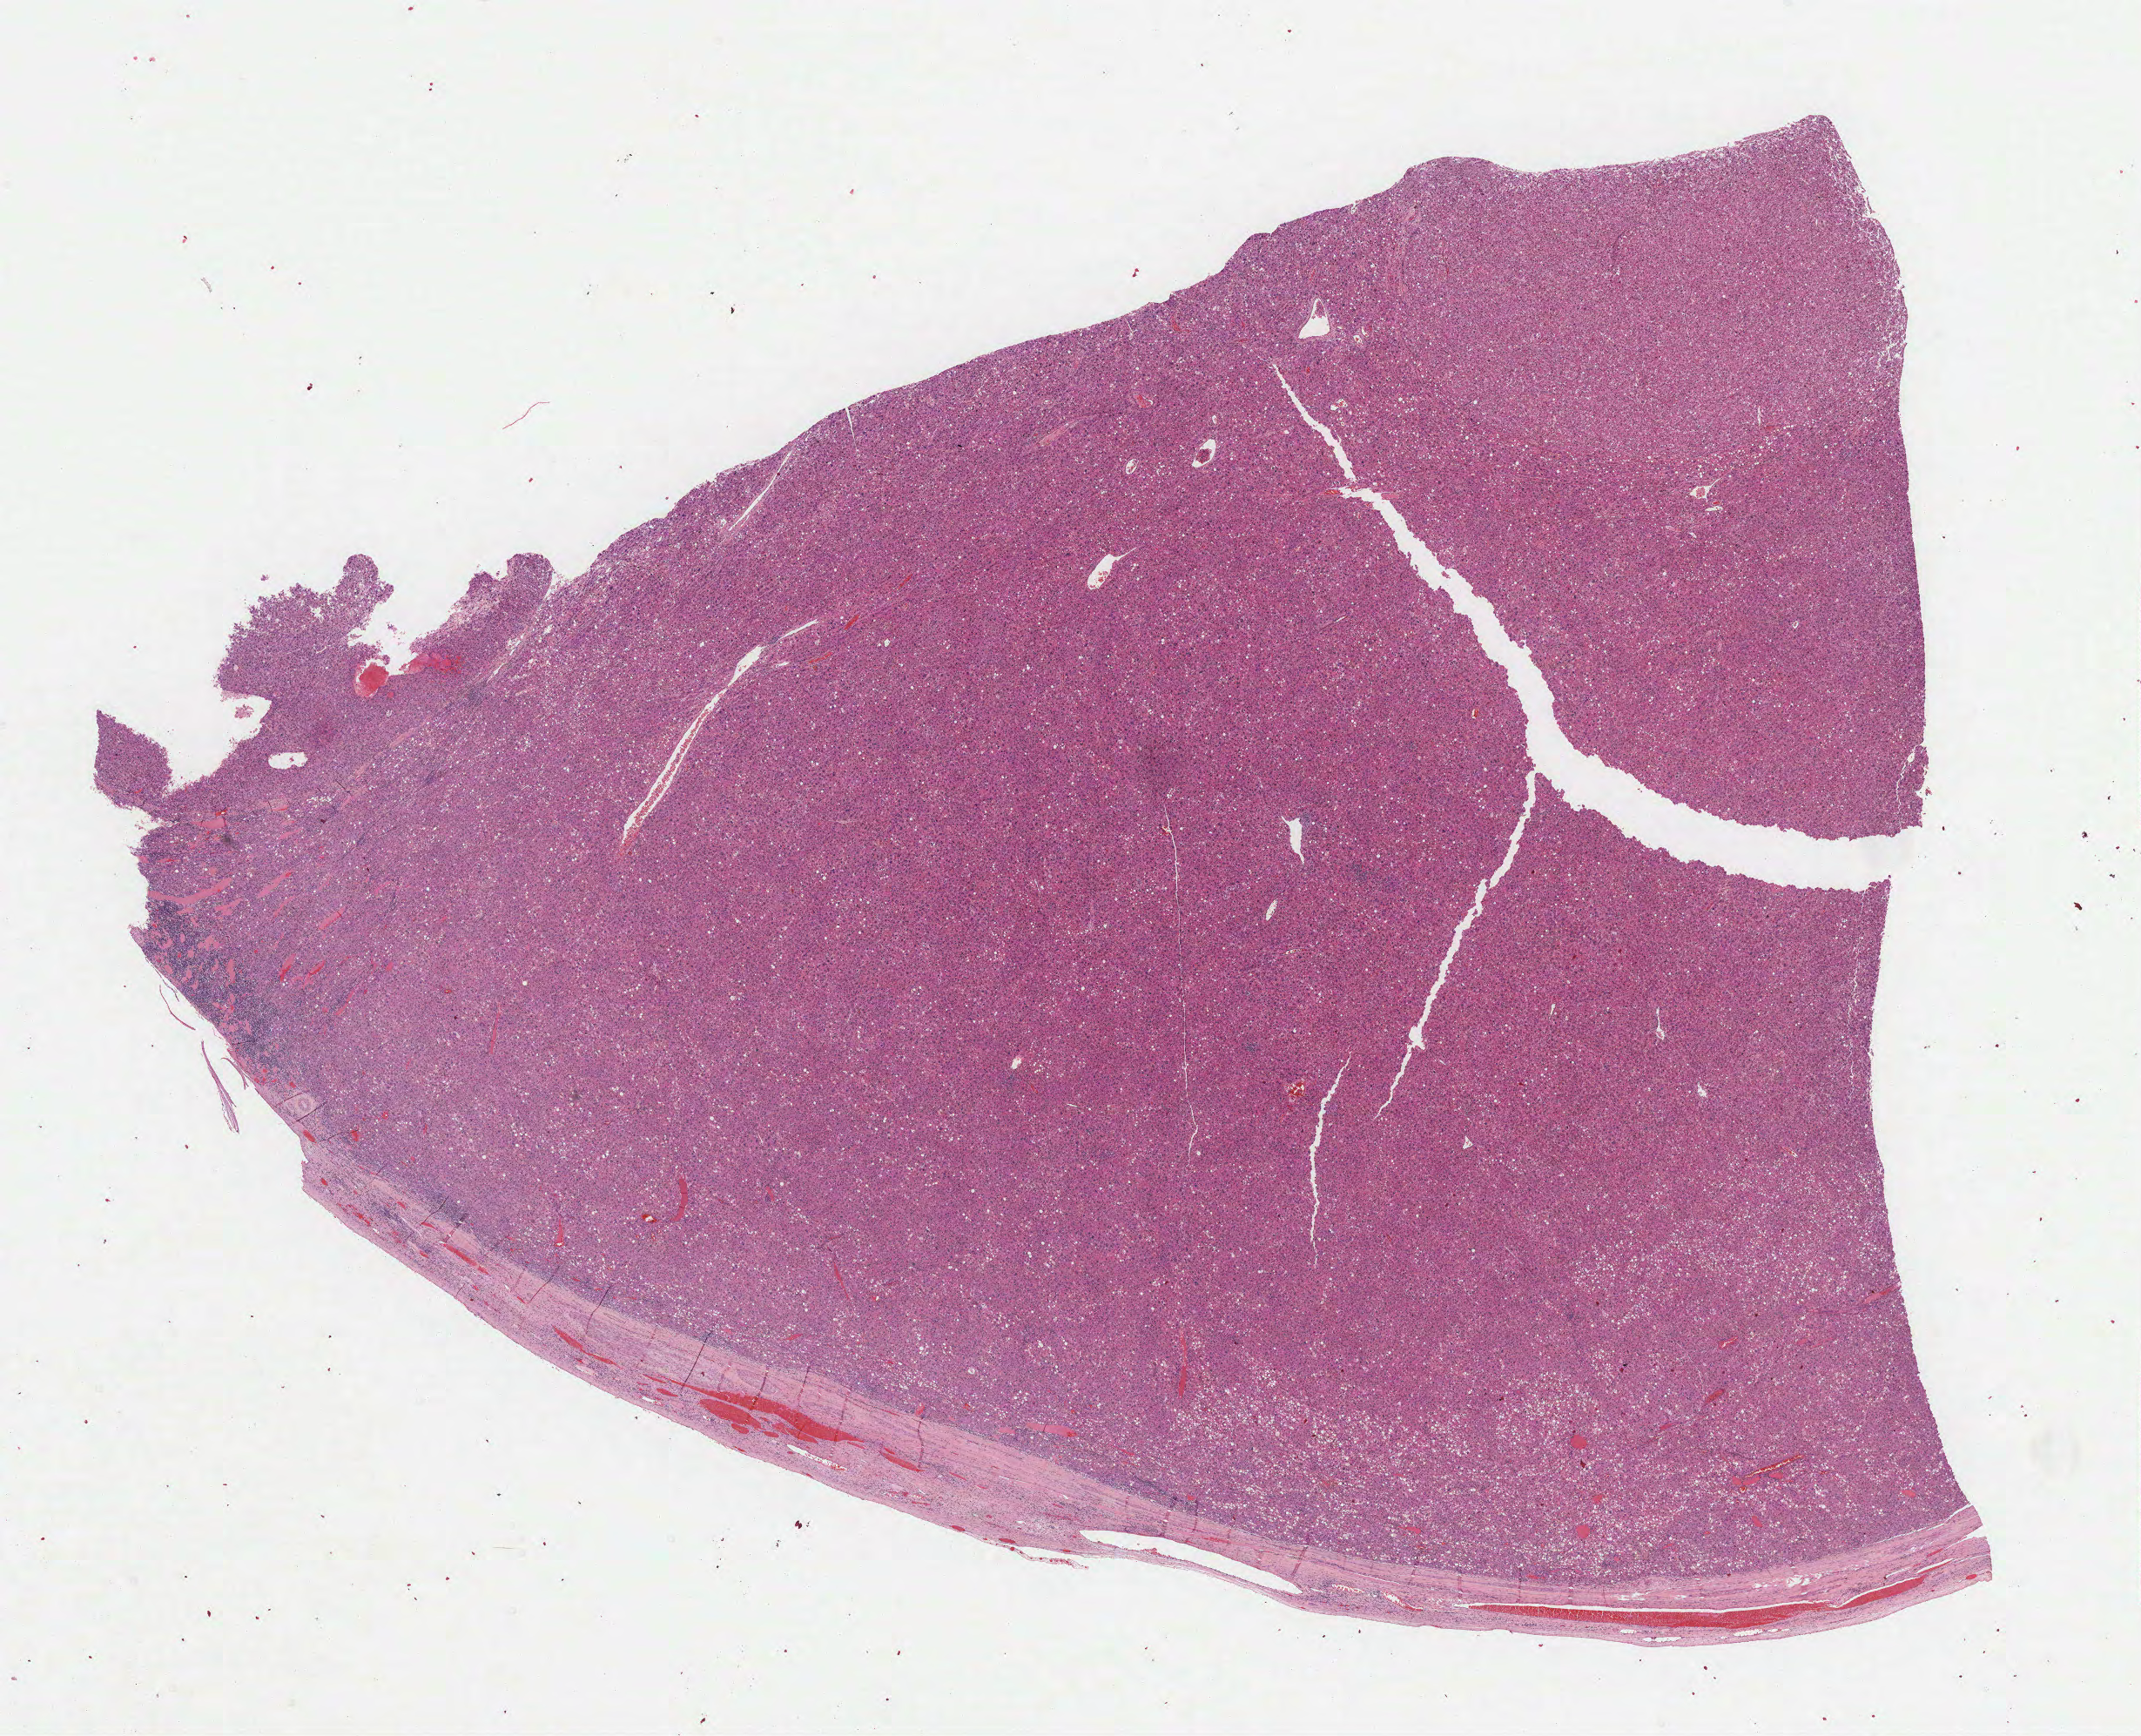
Hematoxylin and eosin (H&E) stained whole-slide image — low-resolution overview of the scanned area, about 19.9 x 16.1 mm (from a 40x scan); FFPE section; primary tumour sample from the liver. Female, age 55 years at initial diagnosis. Histologic grade: G2 (moderately differentiated).
AJCC pathologic stage: I (6th edition). Diagnosis: Hepatocellular carcinoma, NOS.